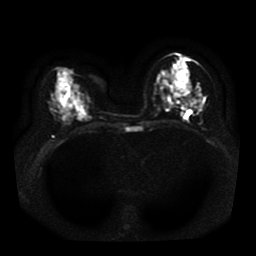
Breast MRI, one axial slice. Position 15 of 41 along the scan axis. Diffusion-weighted series; image 2 of 4 stored at this slice position (different b-values; order by instance number). 1.5 T. 5 mm slice thickness. 256 × 256 image matrix, field of view 330 × 330 mm. Female patient.
Annotated regions visible in this slice (manually delineated by an expert):
- tumour on diffusion-weighted imaging: bounding box (x1, y1, x2, y2) in pixels: (173, 93, 180, 99)